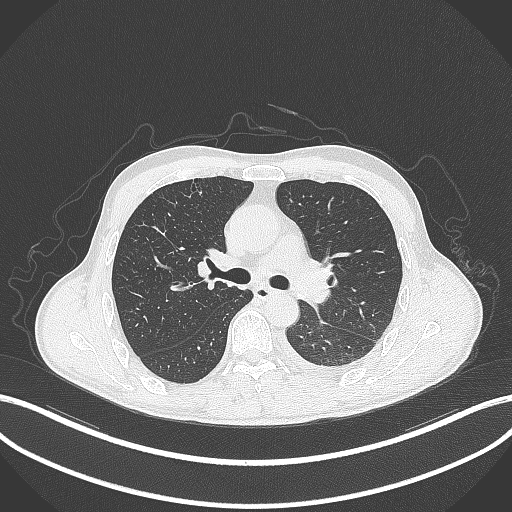
Chest CT, one axial slice; slice 207 of 295 in the series (ordered by position); 120 kVp; lung window (W 1500 / L -600 HU); 1 mm slice thickness; 512 × 512 image matrix, field of view 400 × 400 mm. Patient: male, 47 years. Case-level facts recorded for this patient, not image findings: clinical TNM (as recorded): T3 N1 M1c.
Structures marked on this image (bounding box drawn by a radiologist):
- lung tumour (recorded histology: small cell carcinoma): bounding box [x1, y1, x2, y2] px = [300, 281, 331, 303]